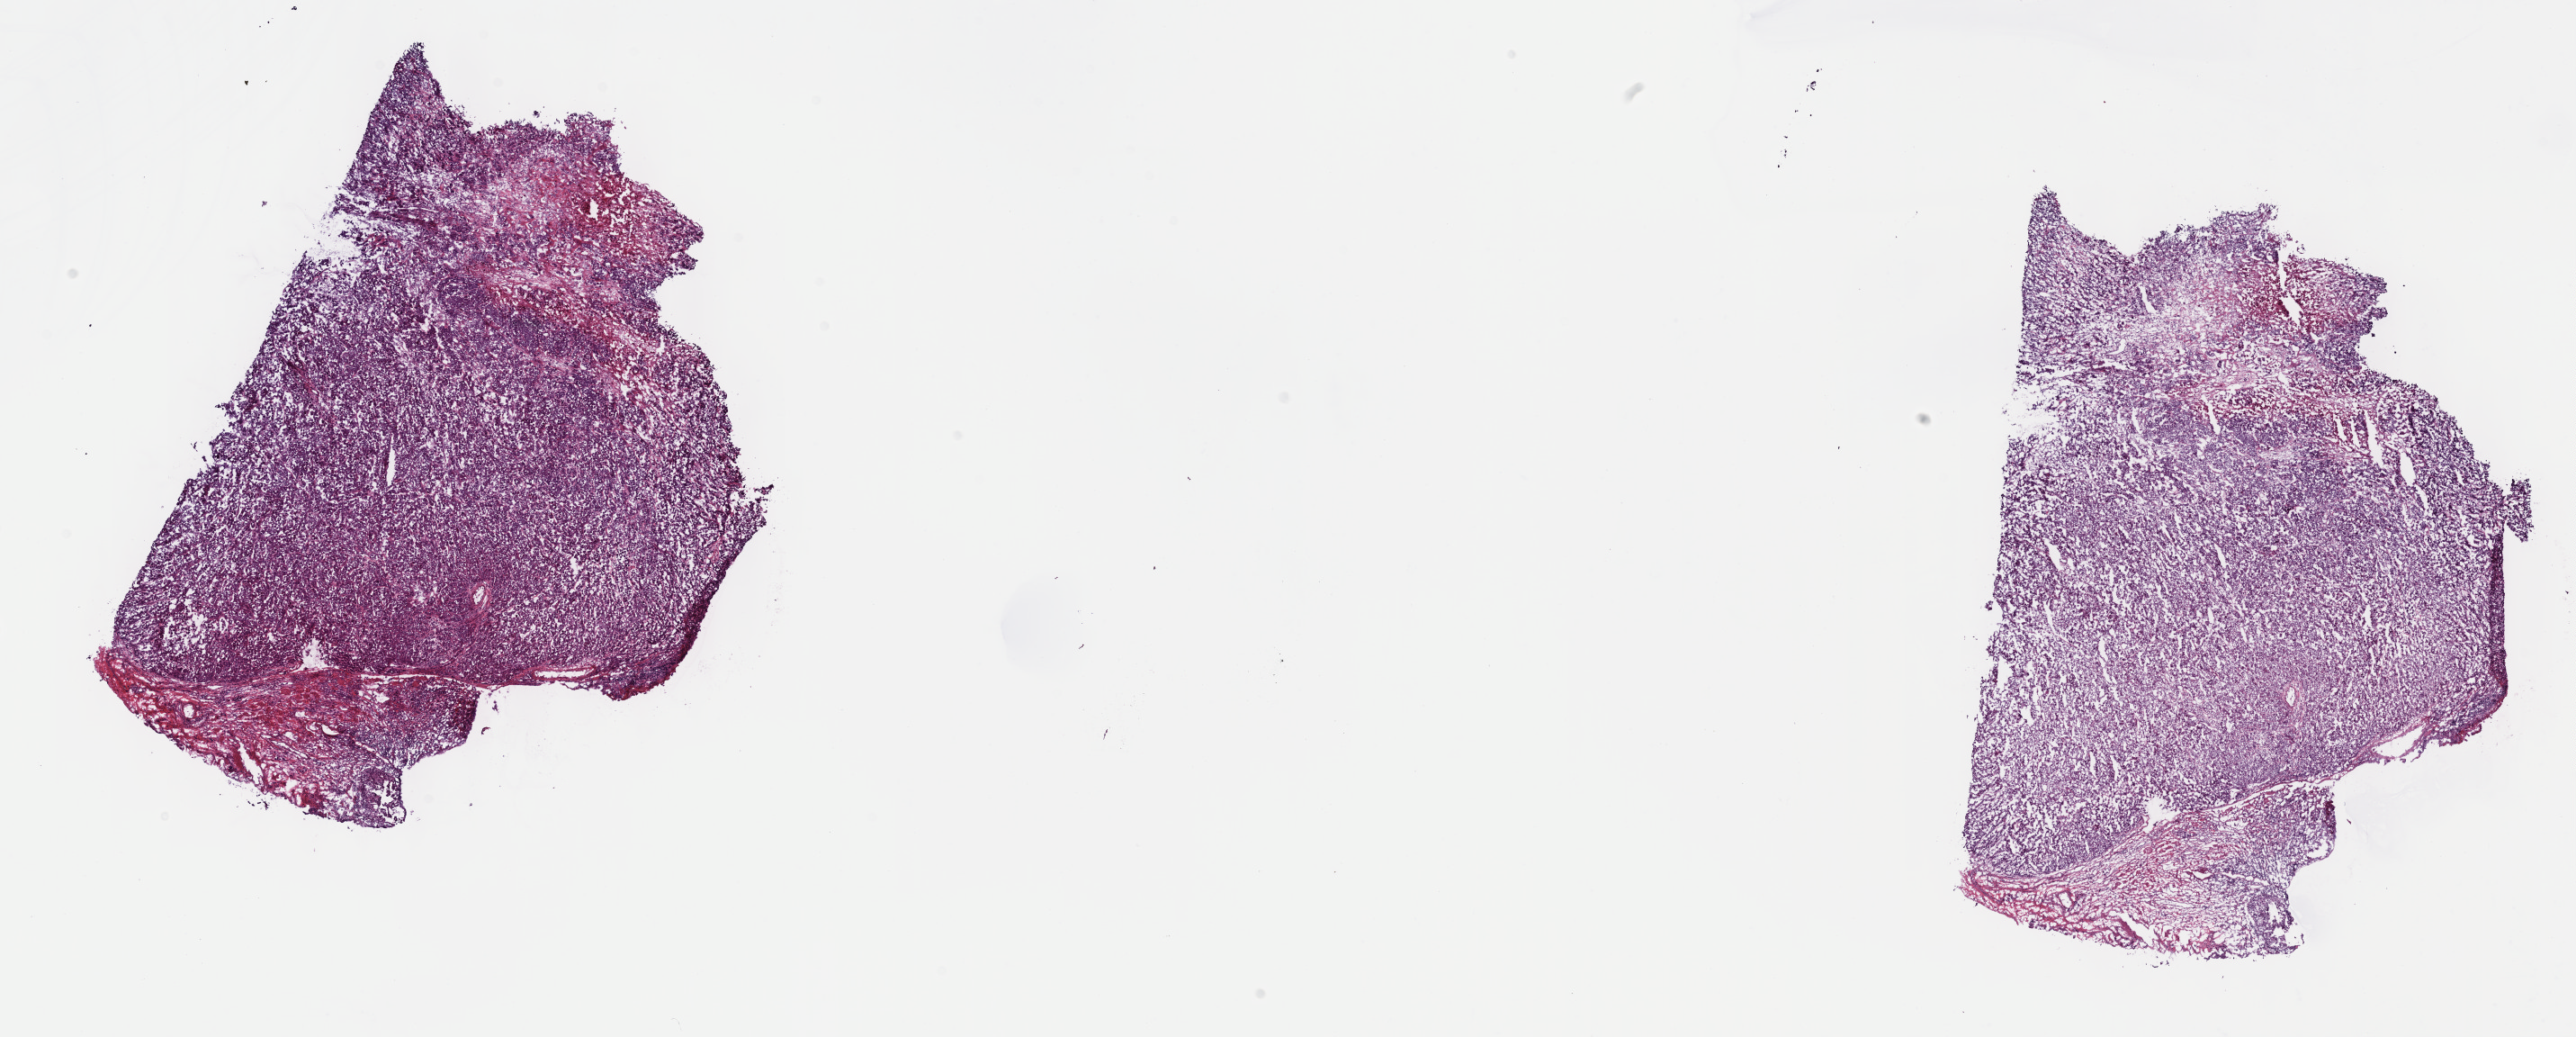
Digitized Hematoxylin and eosin (H&E) stained tissue section (whole slide), low-resolution overview of the scanned area, about 23.2 x 9.3 mm (slide scanned at 40x). Frozen section from the top of the tissue portion. Primary tumour sample from the bladder. Male patient; age at initial diagnosis 61 years. Histologic grade: high grade. Slide review estimates, as recorded: tumour cells 86%, tumour nuclei 93%, normal cells 0%, stromal cells 8%, necrosis 6%. Infiltration values recorded for this section: lymphocyte infiltration 4%, monocyte infiltration 0%, neutrophil infiltration 0%.
Lymph nodes positive (case pathology): 2 of 2 examined. Pathologic diagnosis: Transitional cell carcinoma. AJCC pathologic stage: IV (7th edition).